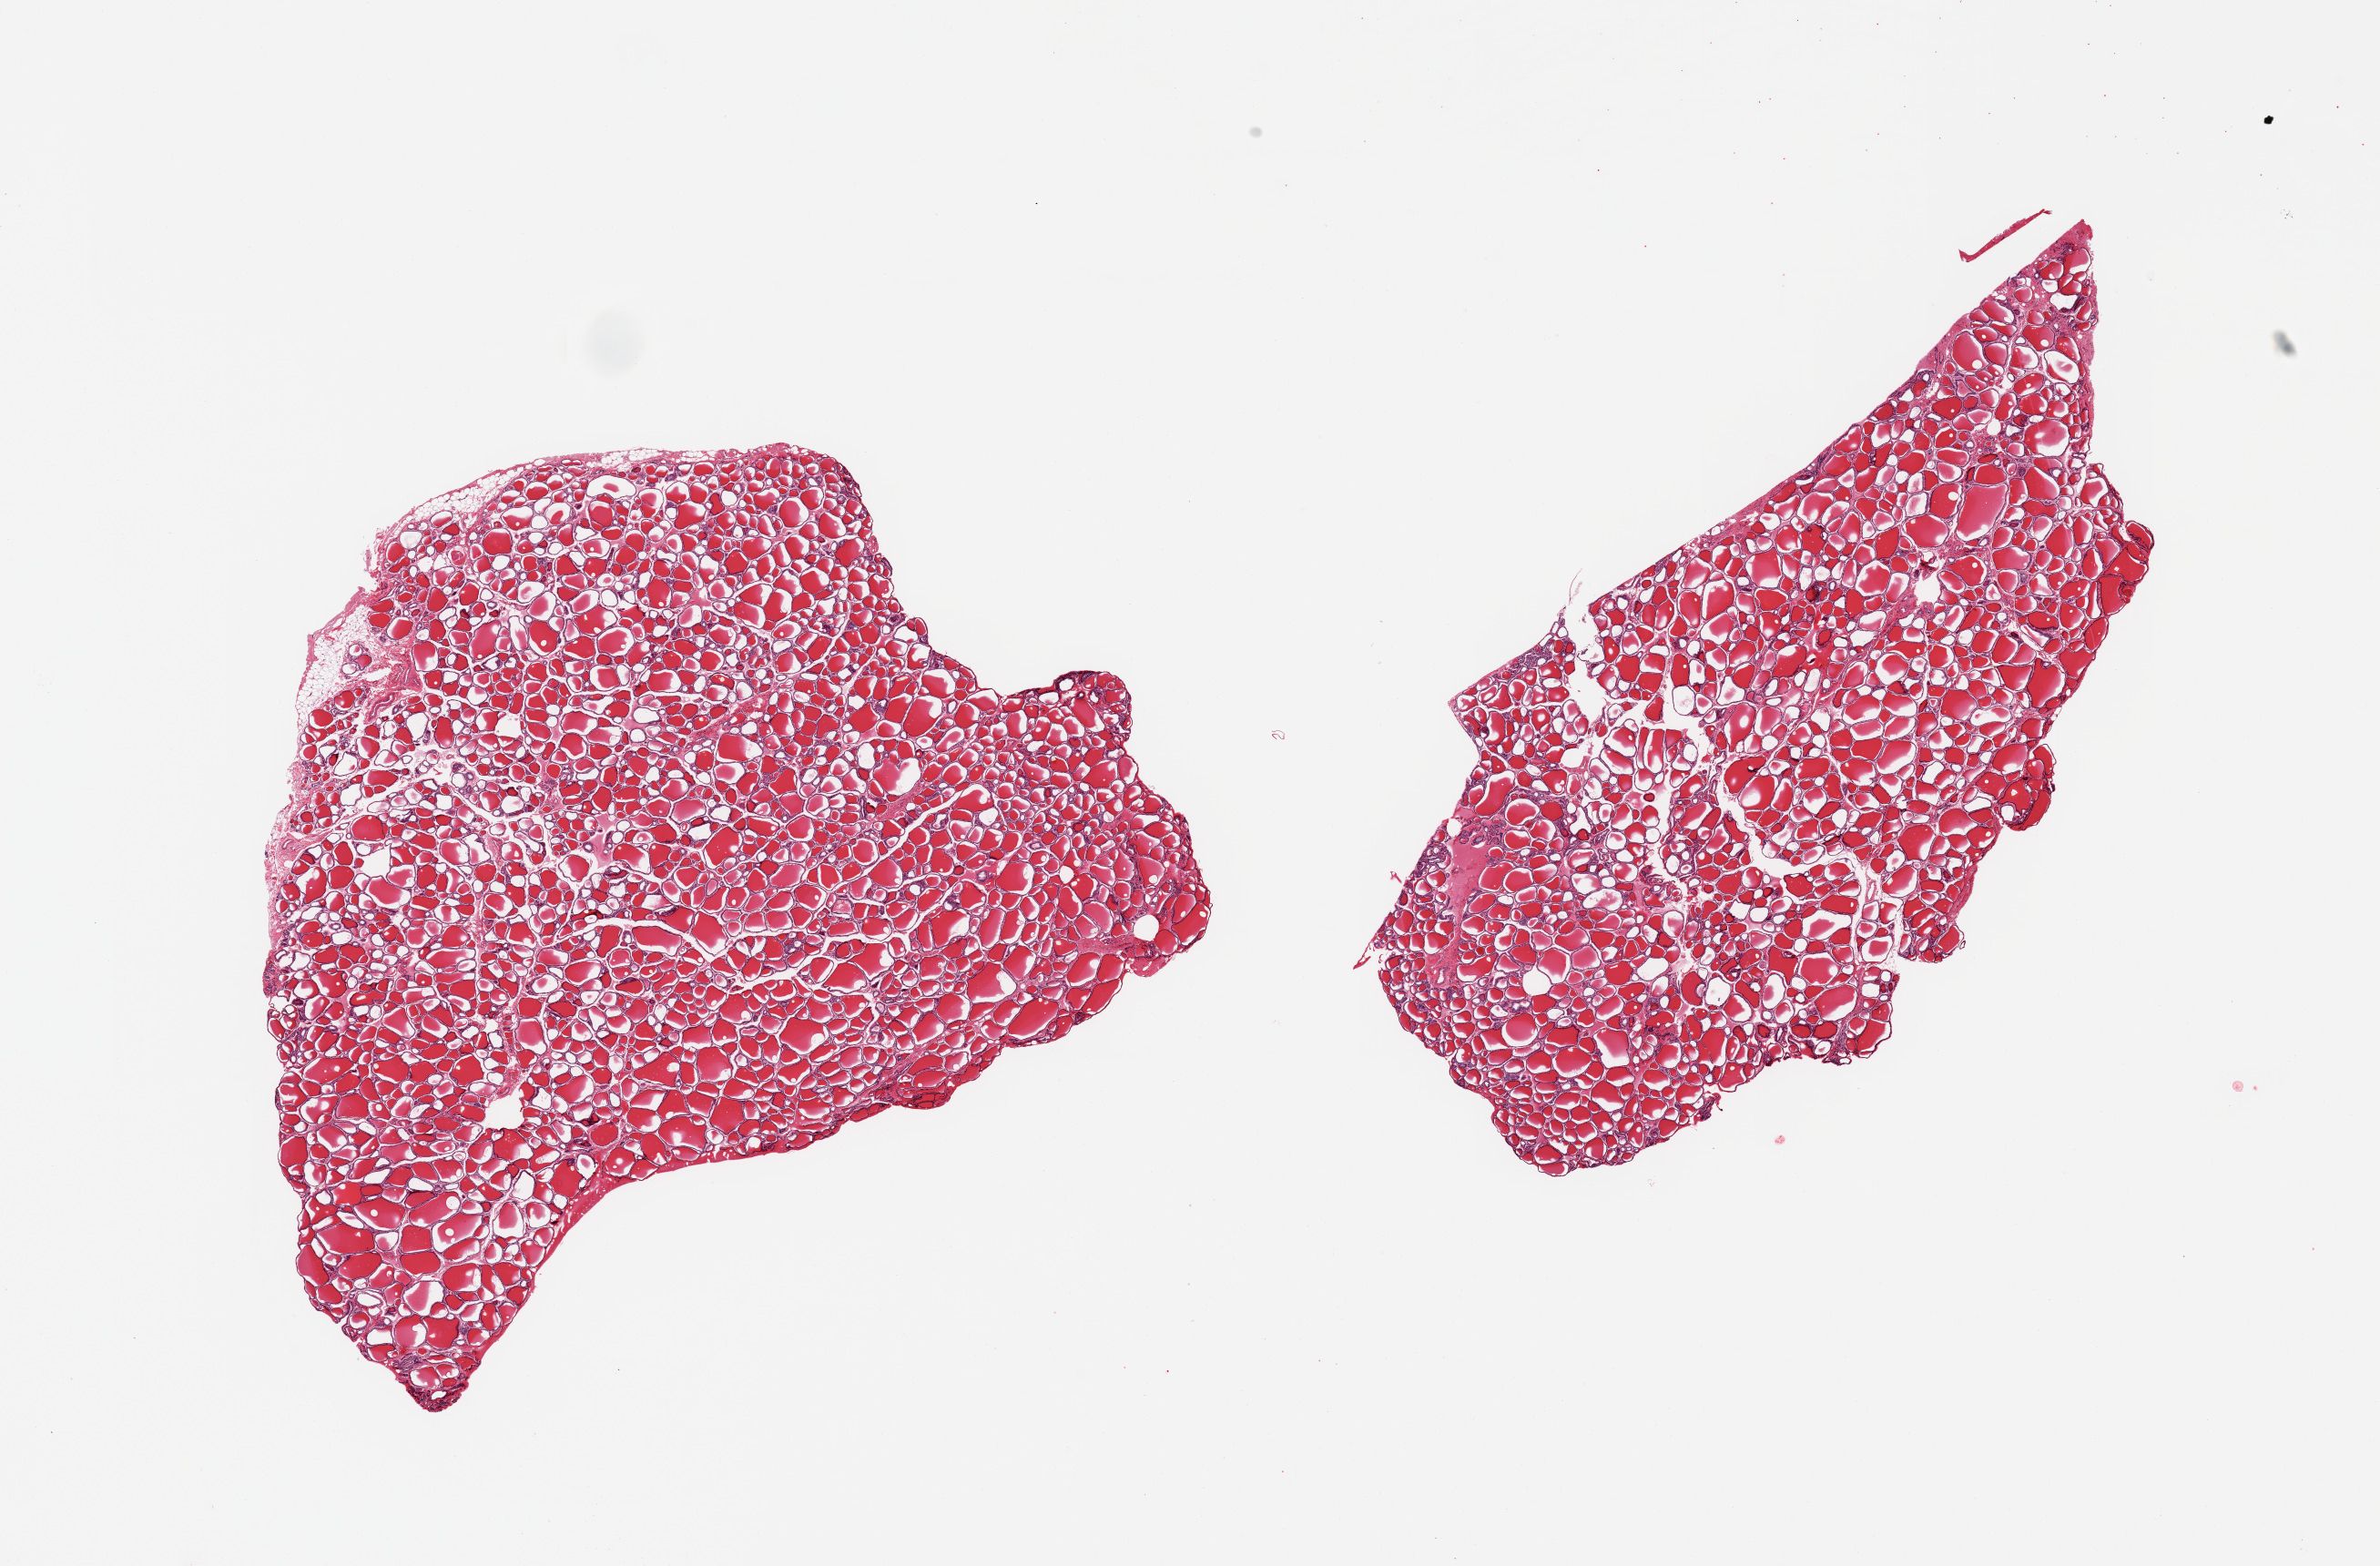
Haematoxylin and eosin whole-slide image, brightfield — whole scanned area (about 20.7 x 13.6 mm, from a 20x scan) shown as a low-resolution overview. PAXgene-fixed, paraffin-embedded tissue. Section of thyroid (target tissue). Tissue donor sample. Donor sex: female.
Pathologist's review note for this sample: 2 pieces, no abnormalities.